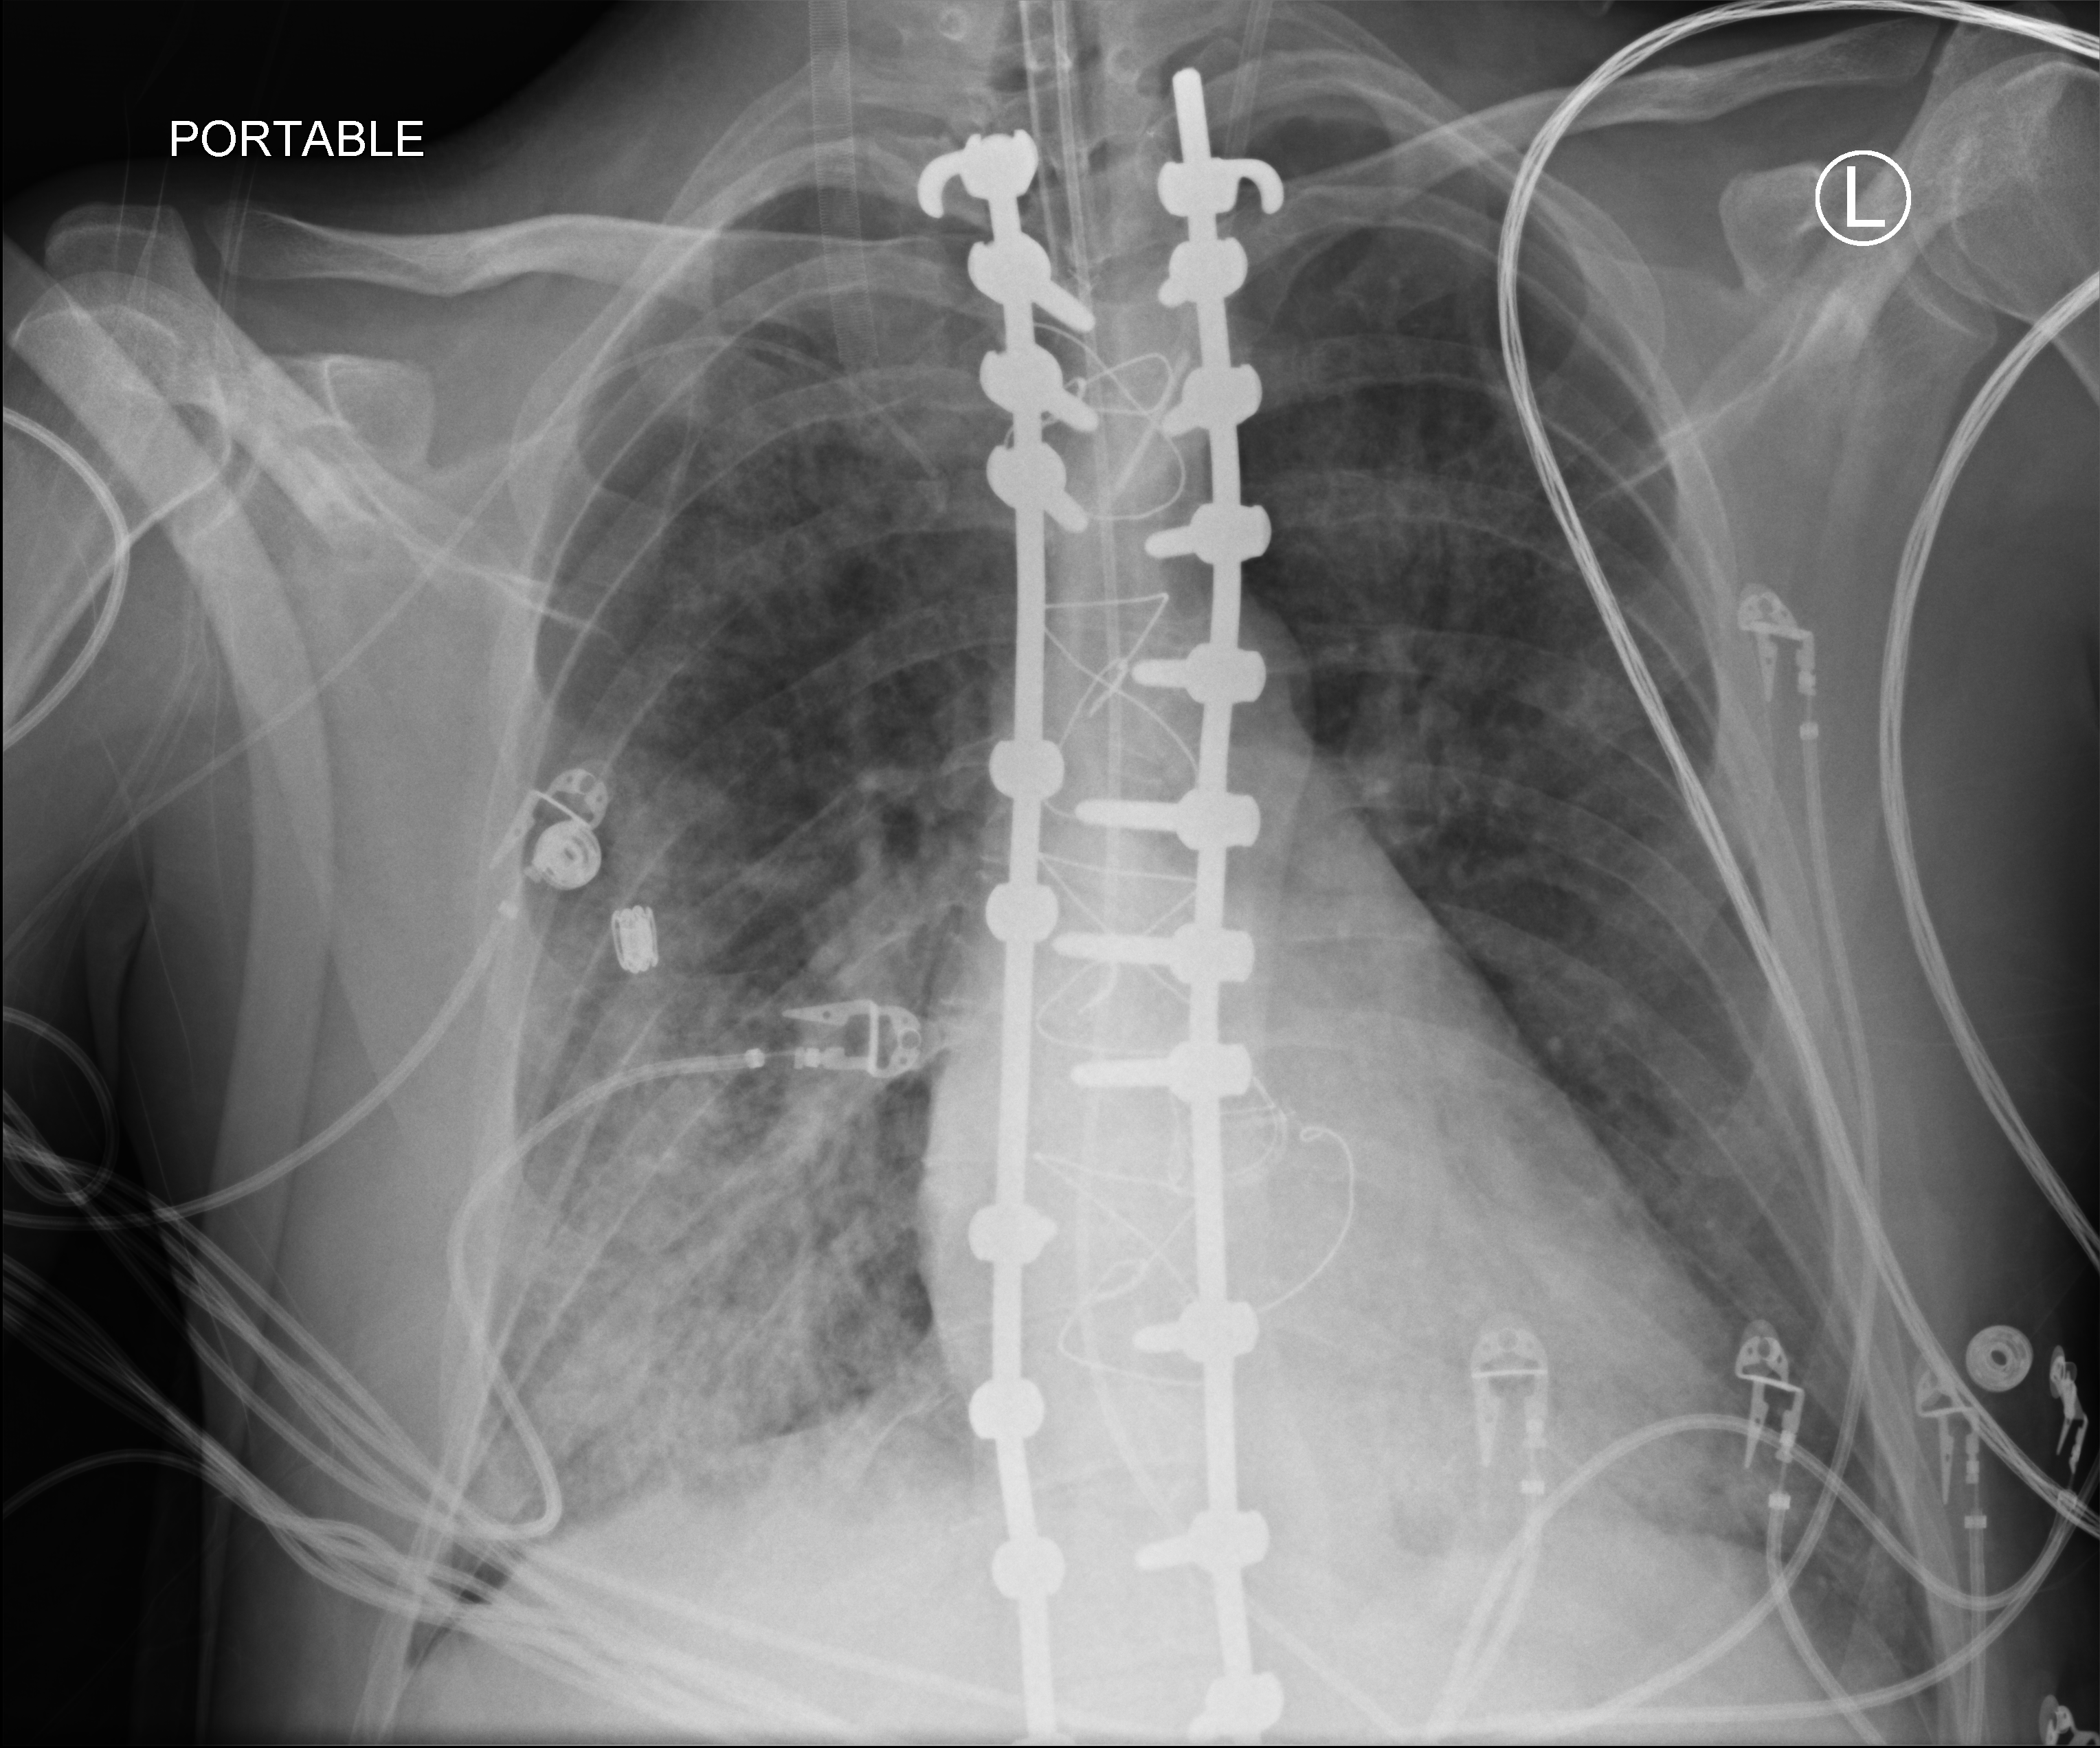
Bedside chest radiograph (computed radiography). Patient hospitalised with COVID-19, aged 18–59 years.
From the hospital-stay record, not from the radiograph (when in the stay this image was taken is not recorded): mechanically ventilated during this hospital stay: yes.